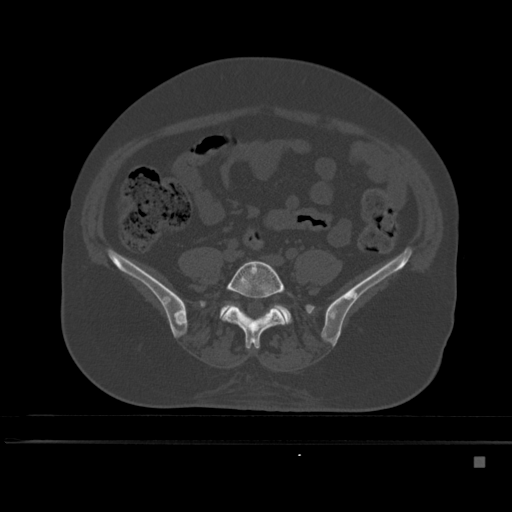
CT including the spine, one axial slice. Slice 107 of 495 in the series (ordered by position). Bone window (W 1800 / L 400 HU). 512 × 512 image matrix, field of view 404 × 404 mm. Patient: female, 33 years. Case-level facts recorded for this patient, not image findings: primary cancer: breast; vertebrae with lytic lesions (as recorded): T1.
Structures marked on this image (semi-automatic segmentation, software-assisted and operator-edited):
- L5 vertebra: bounding box [x1, y1, x2, y2] px = [221, 260, 293, 349]